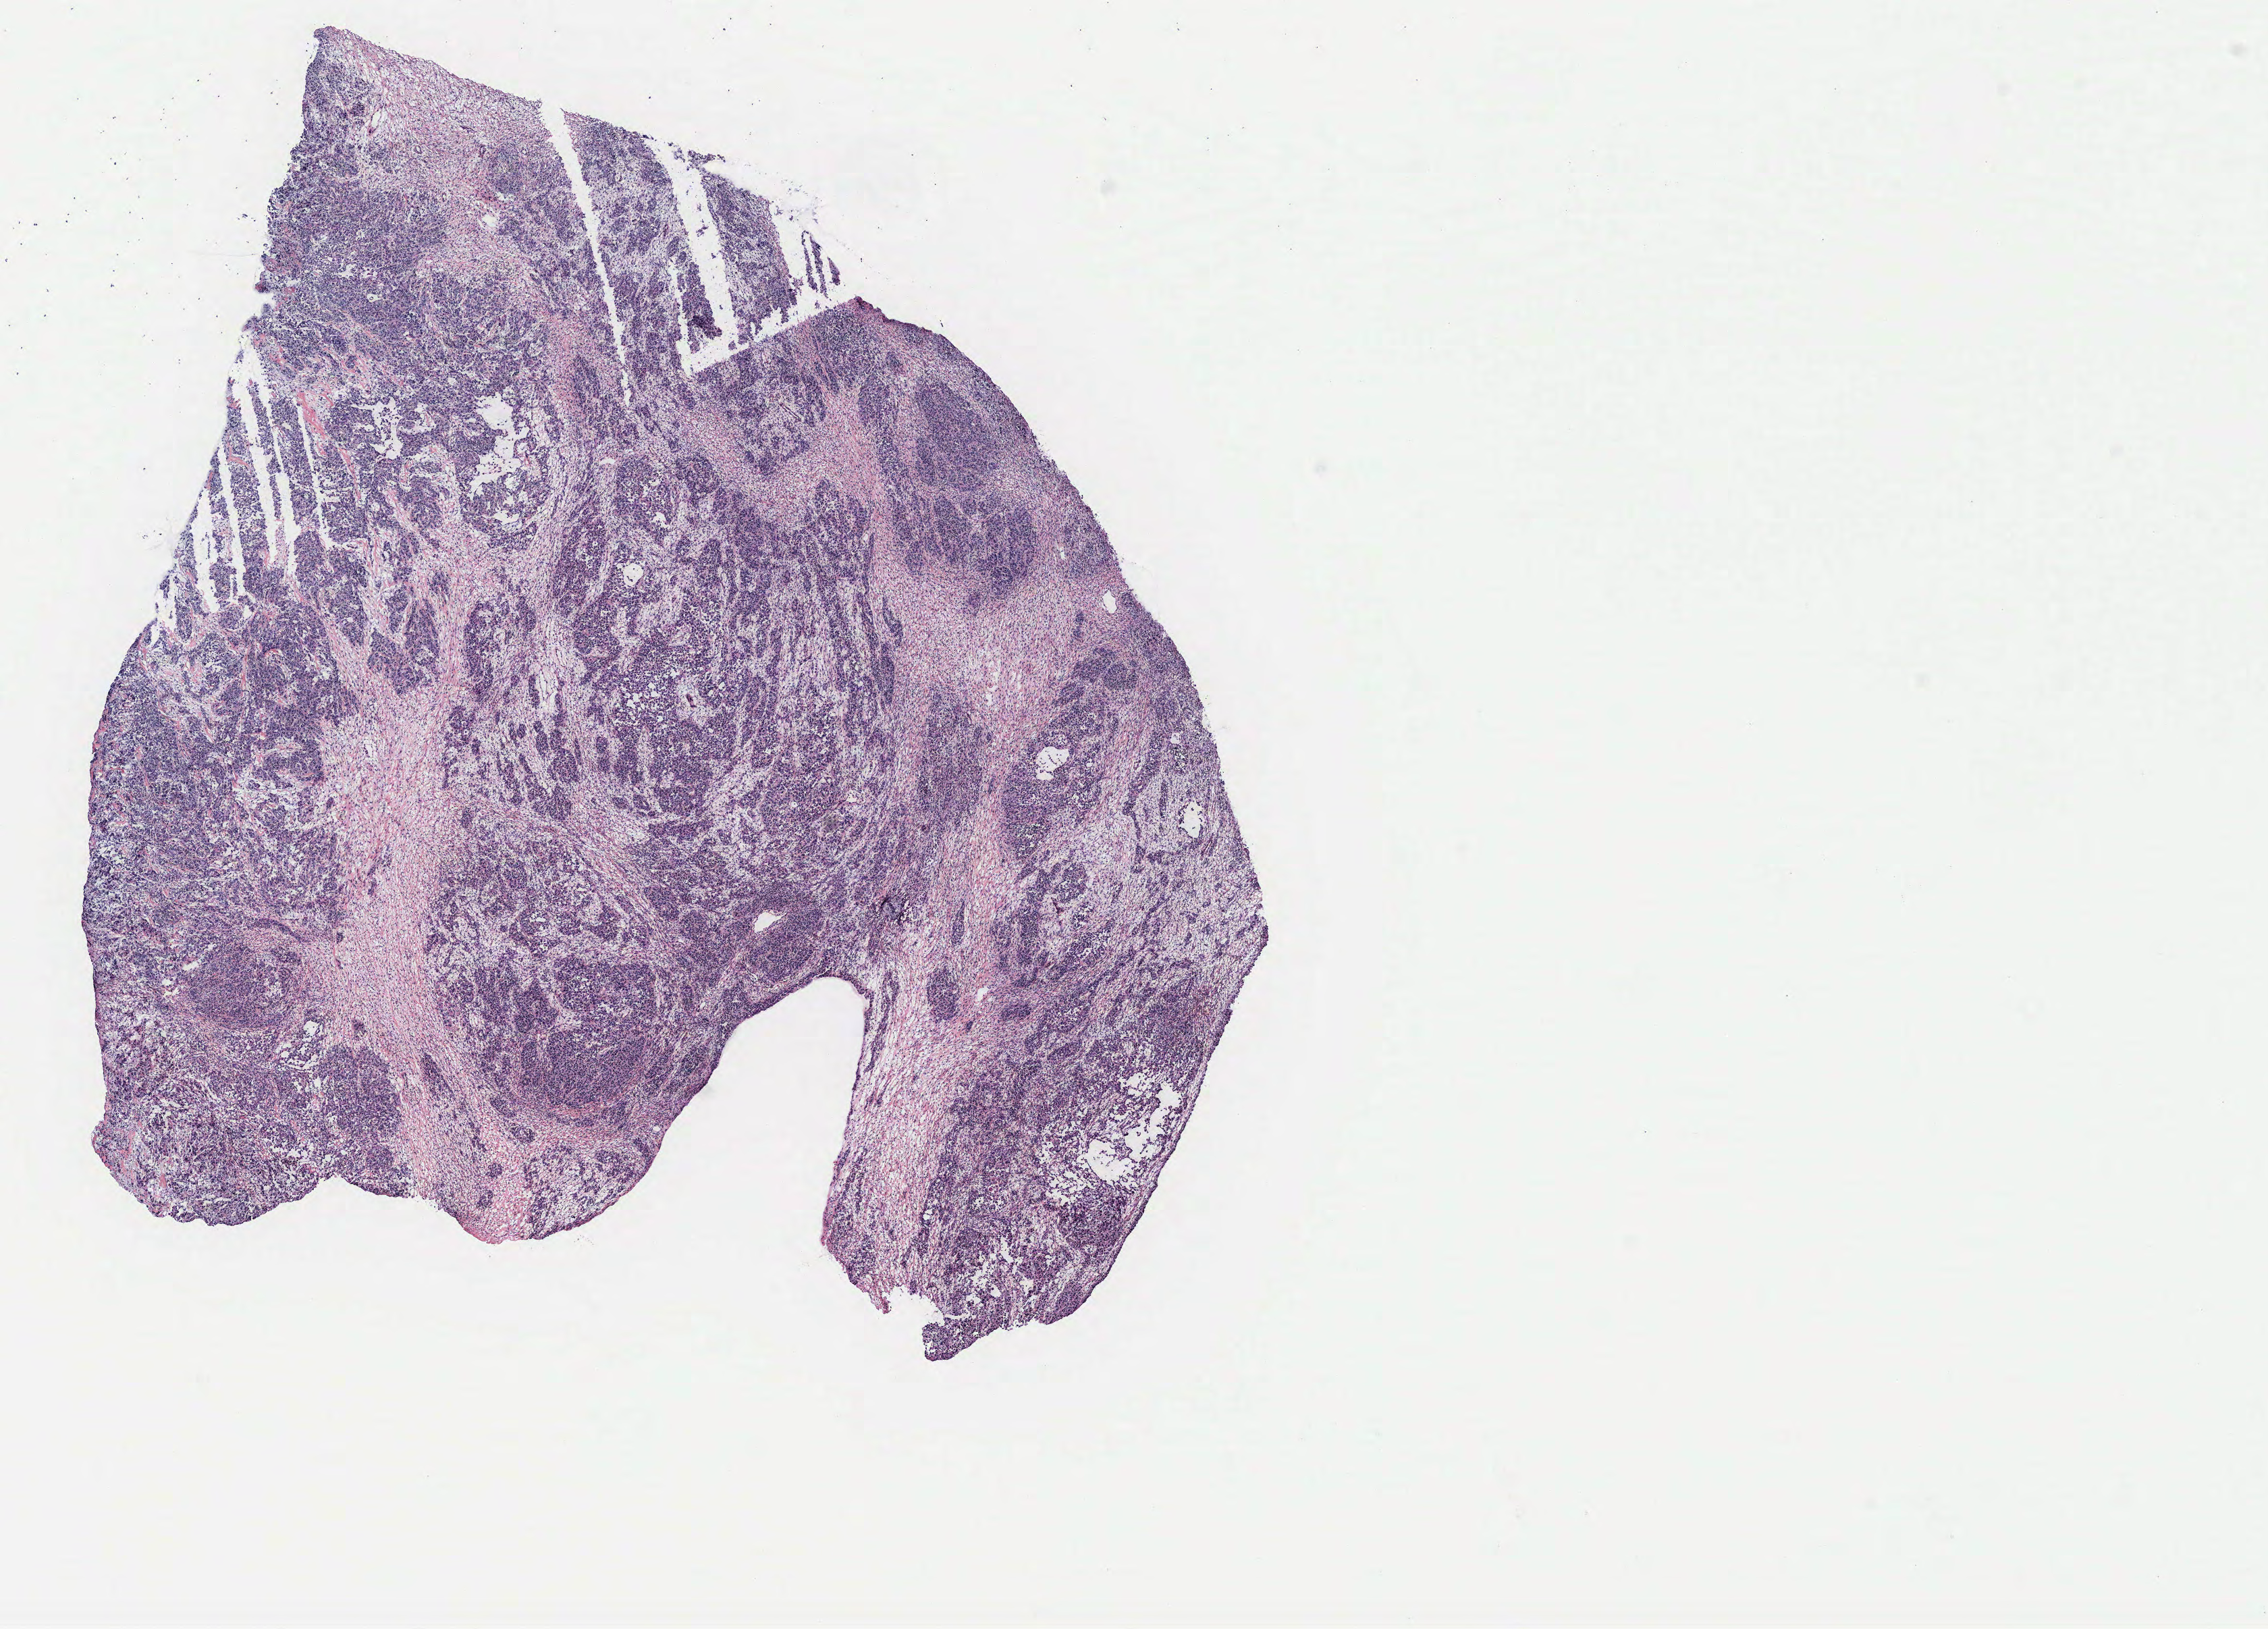
Hematoxylin and eosin (H&E) stained whole-slide image — a low-resolution overview of the entire scanned area, about 13.4 x 9.7 mm (slide scanned at 40x), tumour tissue sample, ovary. Patient: female, age 50 years.
Primary tumour site (as recorded): ovary. Diagnosis: Serous adenocarcinoma, NOS.